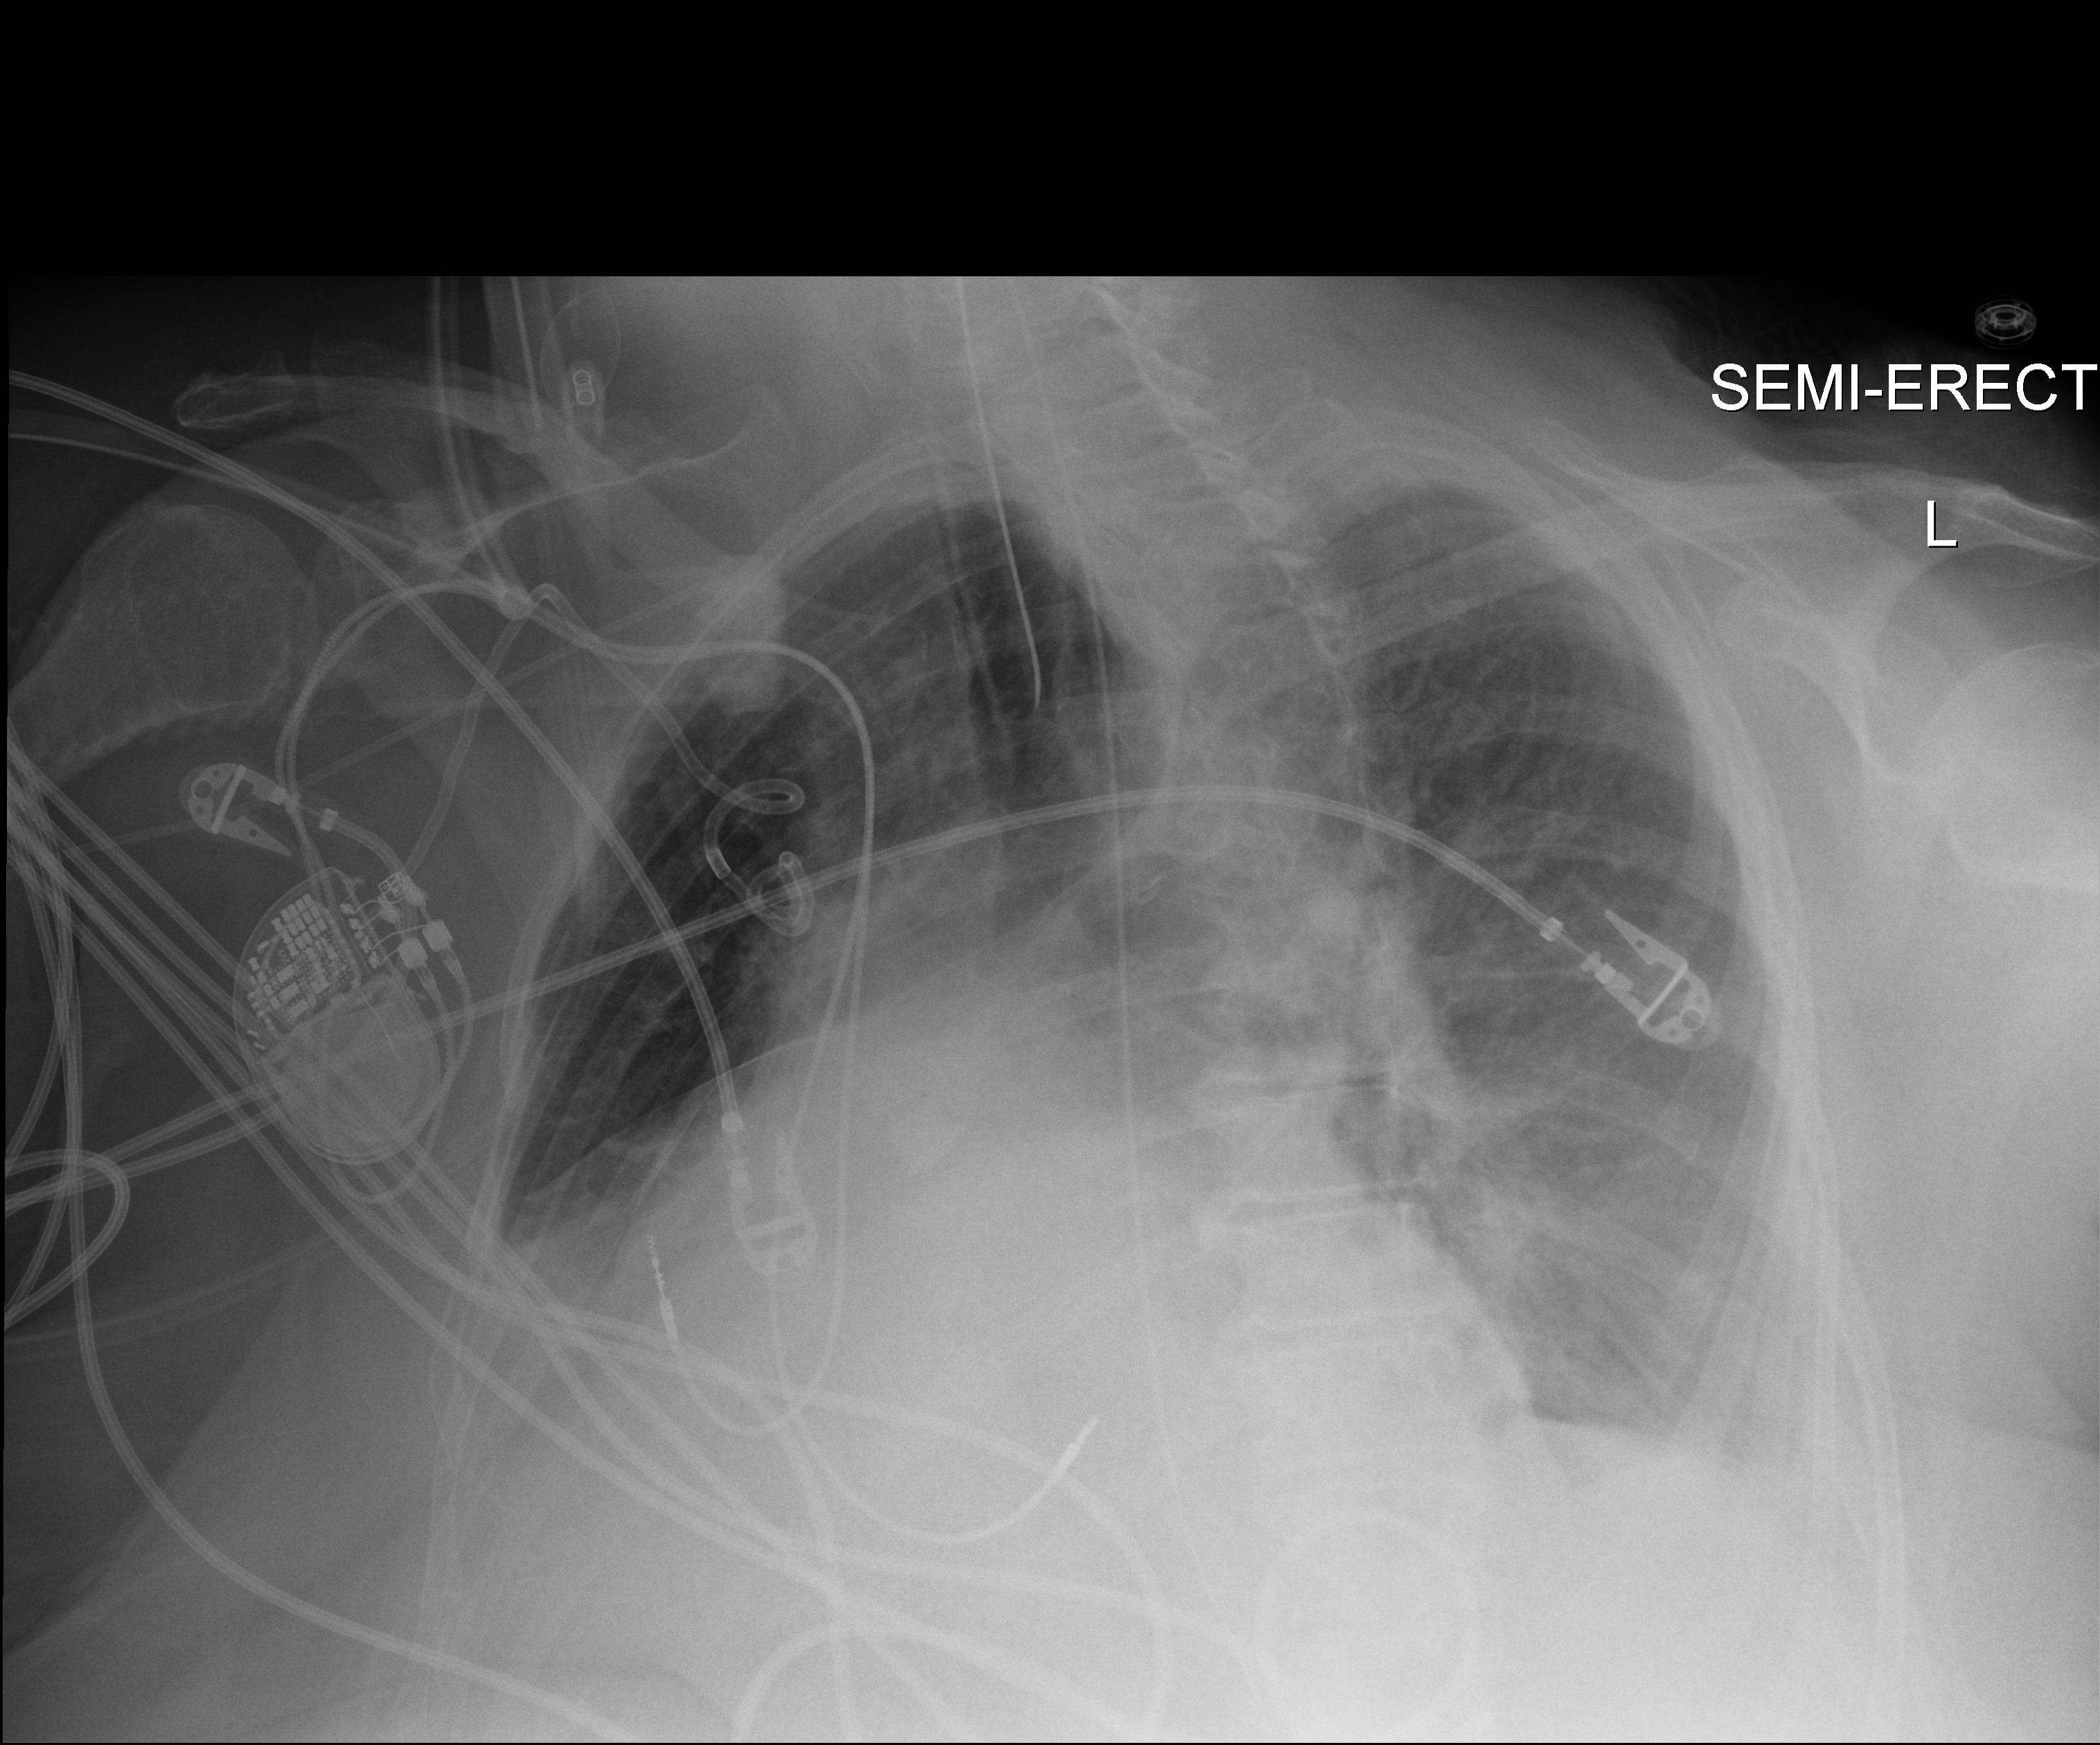
Chest X-ray (portable), anteroposterior (AP) projection. Female patient hospitalised with COVID-19, age 75–90 years.
From the hospital-stay record, not from the radiograph (when in the stay this image was taken is not recorded): mechanically ventilated during this hospital stay: yes; admitted to intensive care during this hospital stay: yes.